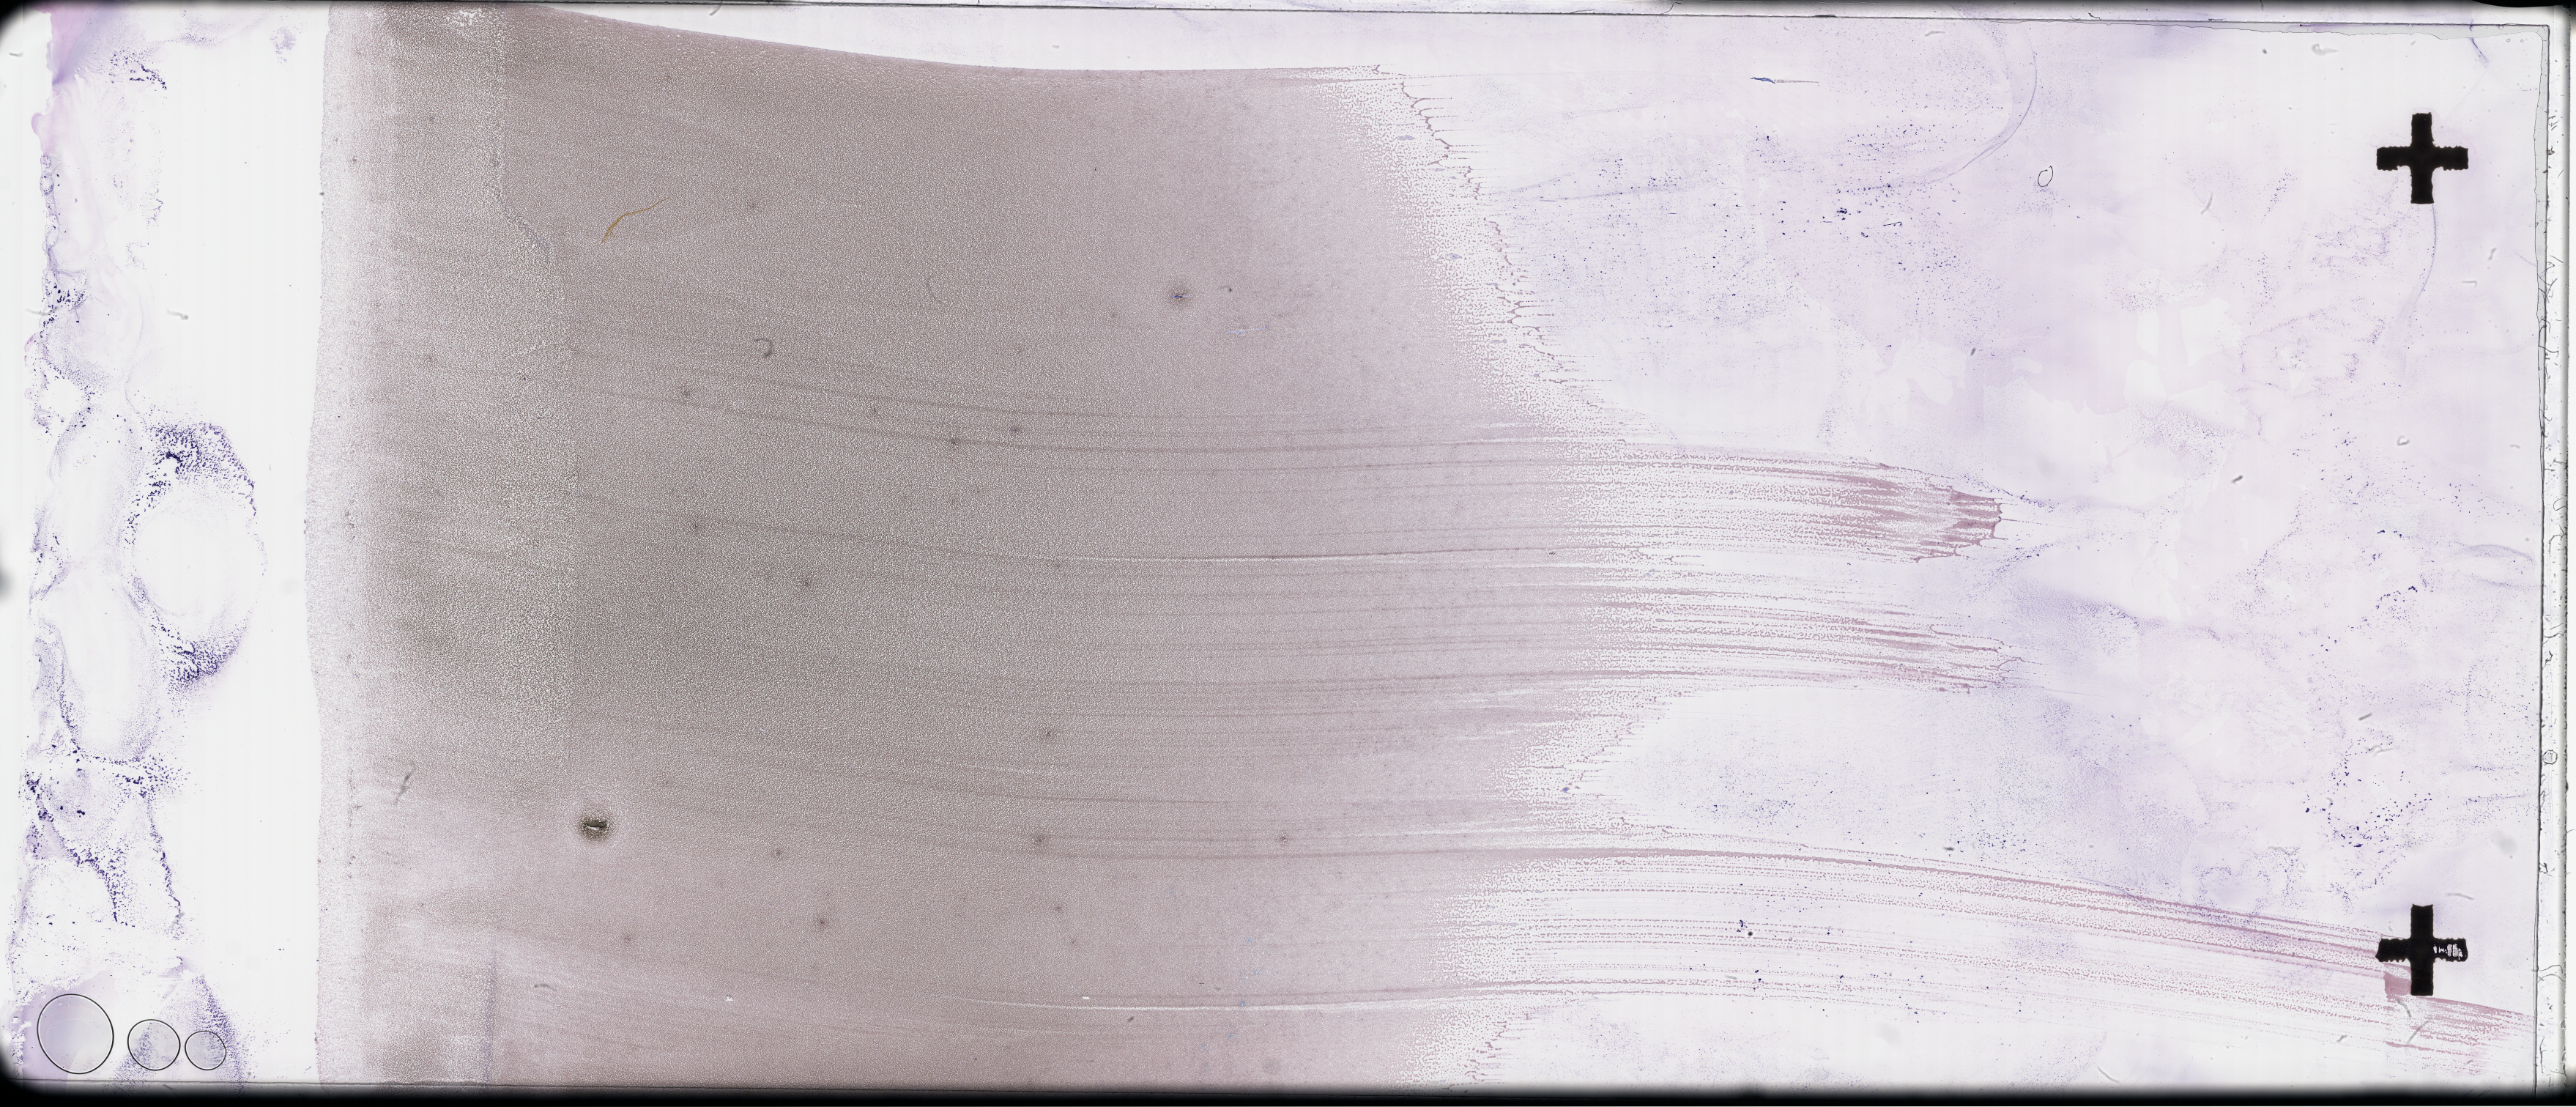
Whole-slide image of a whole blood smear, Wright-Giemsa stain, a low-resolution overview of the entire scanned area, about 56.8 x 24.4 mm, EDTA-anticoagulated smear, collected on treatment. Female patient.
From a patient with: Plasma Cell Myeloma.